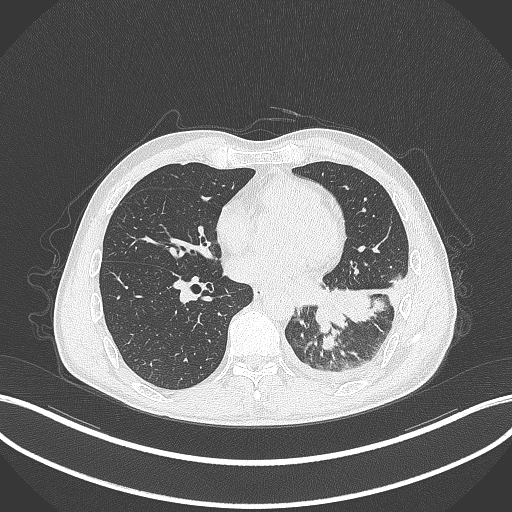
Chest CT, one axial slice; reconstruction kernel B70f; lung window (W 1500 / L -600 HU); 1 mm slice thickness; 512 × 512 image matrix, field of view 400 × 400 mm. Male patient, age 47 years. Case-level facts recorded for this patient, not image findings: clinical TNM (as recorded): T3 N1 M1c.
Annotated regions visible in this slice (bounding box drawn by a radiologist):
- lung tumour (recorded histology: small cell carcinoma): box from (x=311, y=289) to (x=345, y=336) px